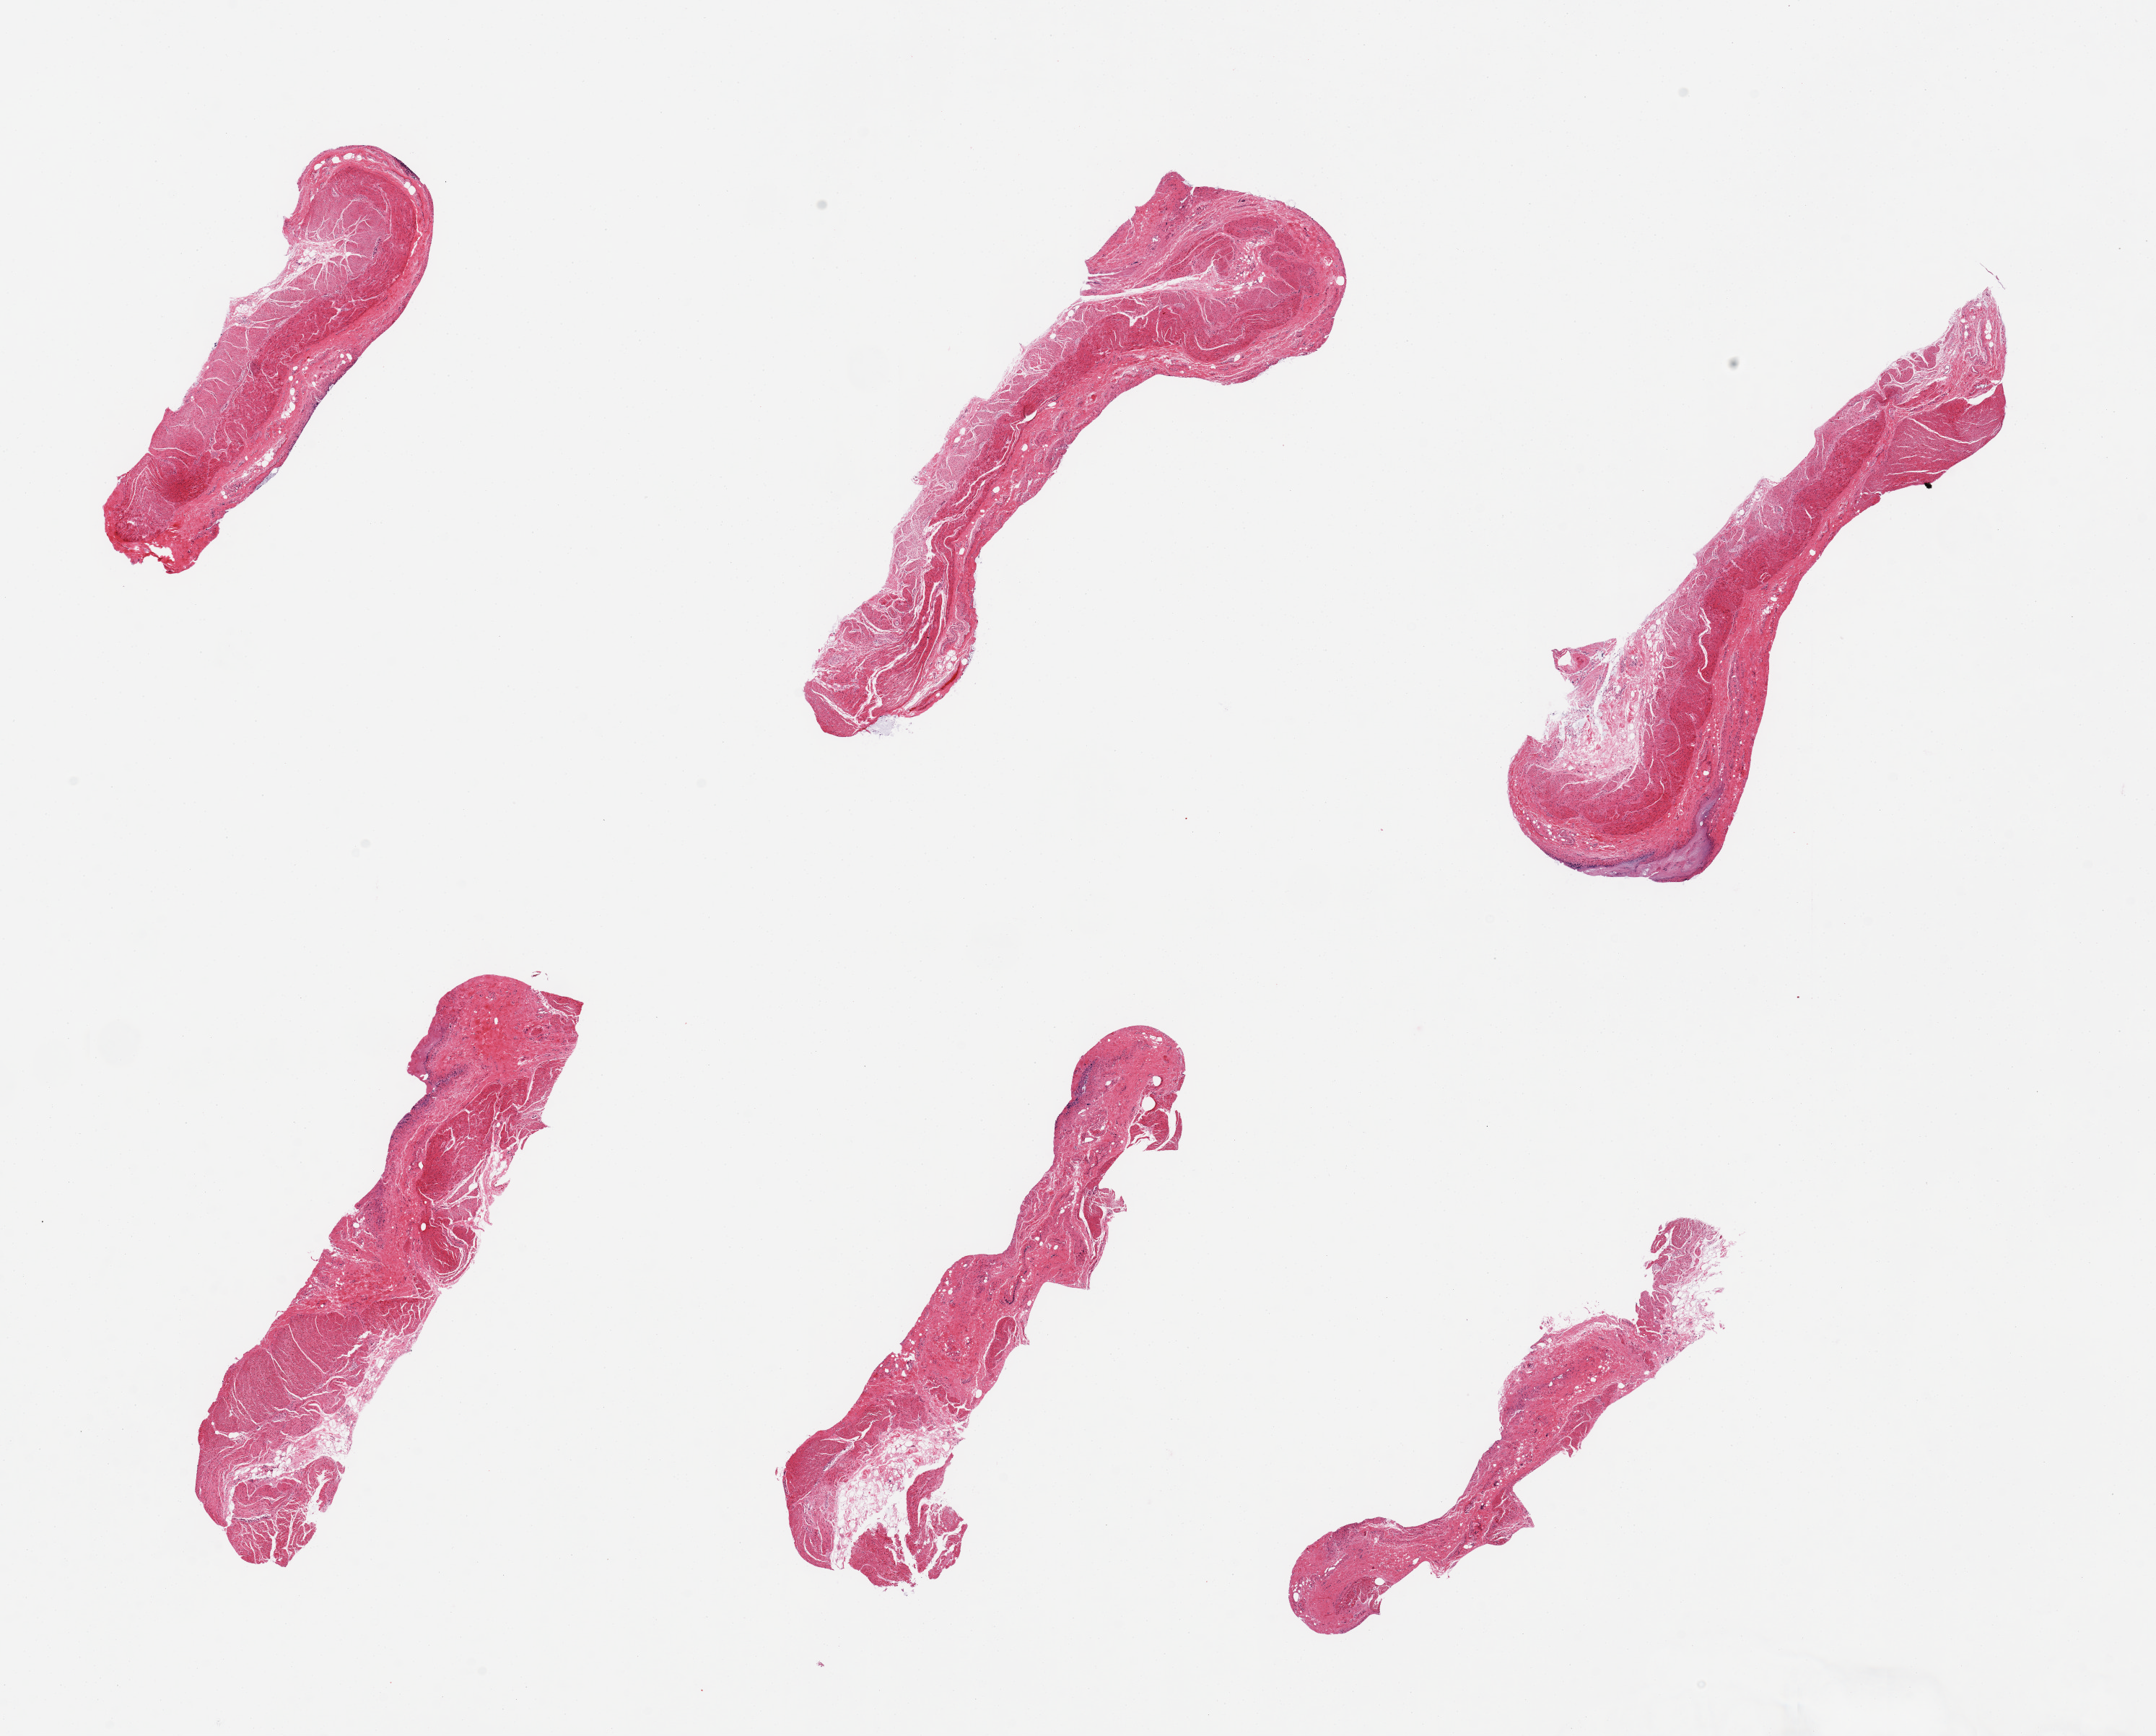
Whole-slide image, haematoxylin and eosin stain, whole scanned area (about 23.6 x 19.0 mm, acquisition: 20x scan) shown as a low-resolution overview, PAXgene-fixed, paraffin-embedded tissue, sampled site (target tissue): sigmoid colon, donor tissue sample. Donor sex: male.
- reviewer comment on this tissue sample: 6 pieces; 20-30% fibrous stroma (submucosa) in all